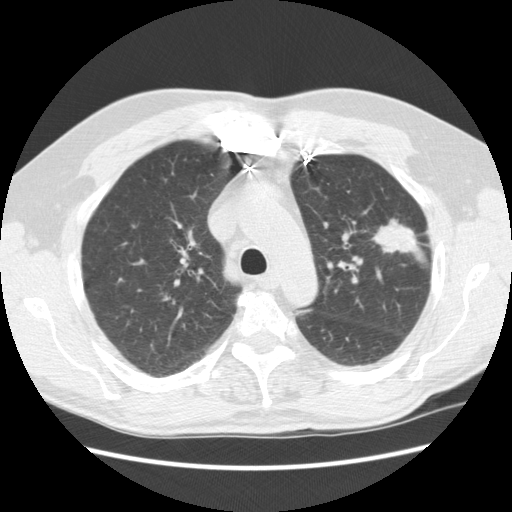
Chest CT (low-dose screening protocol), one axial image. Baseline annual screen. Lung window (W 1500 / L -600 HU). 2.5 mm slice thickness. Standard (soft-tissue) reconstruction kernel (STANDARD). Slice 173 of 231 in the series. Male participant, aged 72 years at enrolment. Former smoker at enrolment.
• Lesion marked by an expert reader, bounding box <352,203,428,260> (left, top, right, bottom; pixels).
• Screening reader's record for this exam (one nodule recorded; not confirmed to be the boxed lesion): non-calcified nodule or mass ≥4 mm, left upper lobe, 25 × 18 mm, spiculated (stellate) margins, soft tissue attenuation.
• Participant outcome: lung cancer diagnosed 35 days after this screen — adenocarcinoma, NOS, left upper lobe, well differentiated (G1), stage IIIB (AJCC 6th edition), 25 mm at pathology.